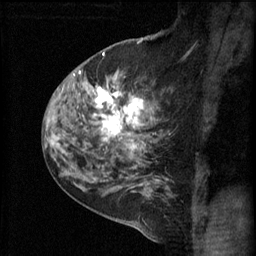
Breast MRI (dynamic contrast-enhanced), one sagittal slice; slice 39 of 60 in the series (ordered by position); 3 images stored at this slice position (order not interpretable as contrast timing); 1.5 T; TE 4.2 ms, TR 11 ms; 2.3 mm slice thickness; 256 × 256 image matrix. Female patient, age 52 years.
Structures marked on this image (semi-automatic segmentation, software-assisted and operator-edited):
- analysis volume of interest (the breast-tissue region the enhancement analysis was run in; not a lesion): box from (x=86, y=76) to (x=165, y=157) px
- tumour enhancement mask (voxels above the 70 % enhancement threshold inside the analysis volume of interest): (x=93, y=80)–(x=144, y=153)